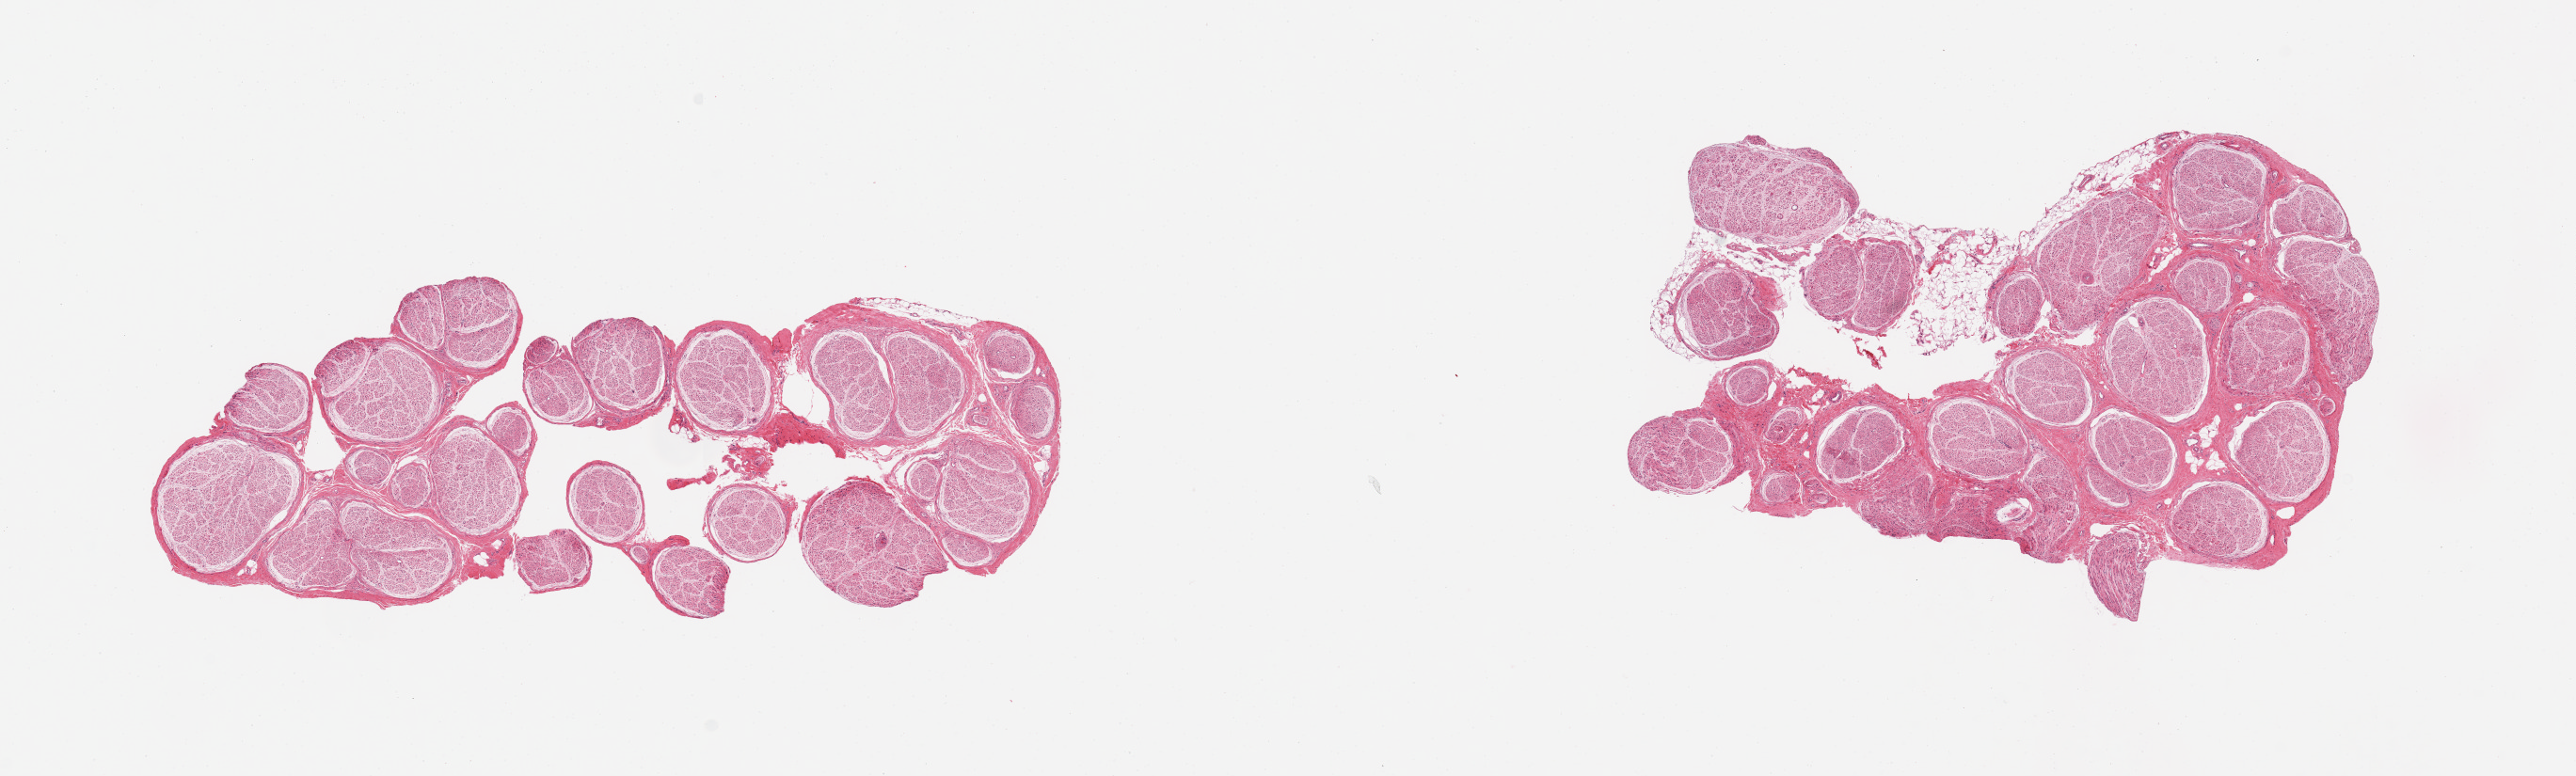
Digitized H&E-stained section, brightfield, low-resolution overview of the scanned area, about 21.7 x 6.5 mm, PAXgene-fixed, paraffin-embedded tissue, target tissue: tibial nerve, donor tissue sample. Donor sex: male.
Review note (as recorded): 2 pieces; well trimmed with minimal external fat.